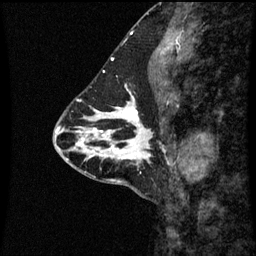
Breast MRI (dynamic contrast-enhanced), one sagittal slice; slice 25 of 60 in the series (ordered by position); dynamic contrast-enhanced series, image 2 of 3 at this slice position (ordered by acquisition); 1.5 T; TE 4.2 ms, TR 8.9 ms; 2 mm slice thickness; 256 × 256 image matrix. Female patient, age 43 years. Case-level facts recorded for this patient, not image findings: setting: breast cancer imaged before/during neoadjuvant chemotherapy; receptor status: HR-positive, HER2-negative.
Annotated regions visible in this slice (semi-automatic segmentation, software-assisted and operator-edited):
- analysis volume of interest (the breast-tissue region the enhancement analysis was run in; not a lesion): box from (x=110, y=100) to (x=170, y=163) px
- tumour enhancement mask (voxels above the 70 % enhancement threshold inside the analysis volume of interest): (x=110, y=100)–(x=150, y=161)